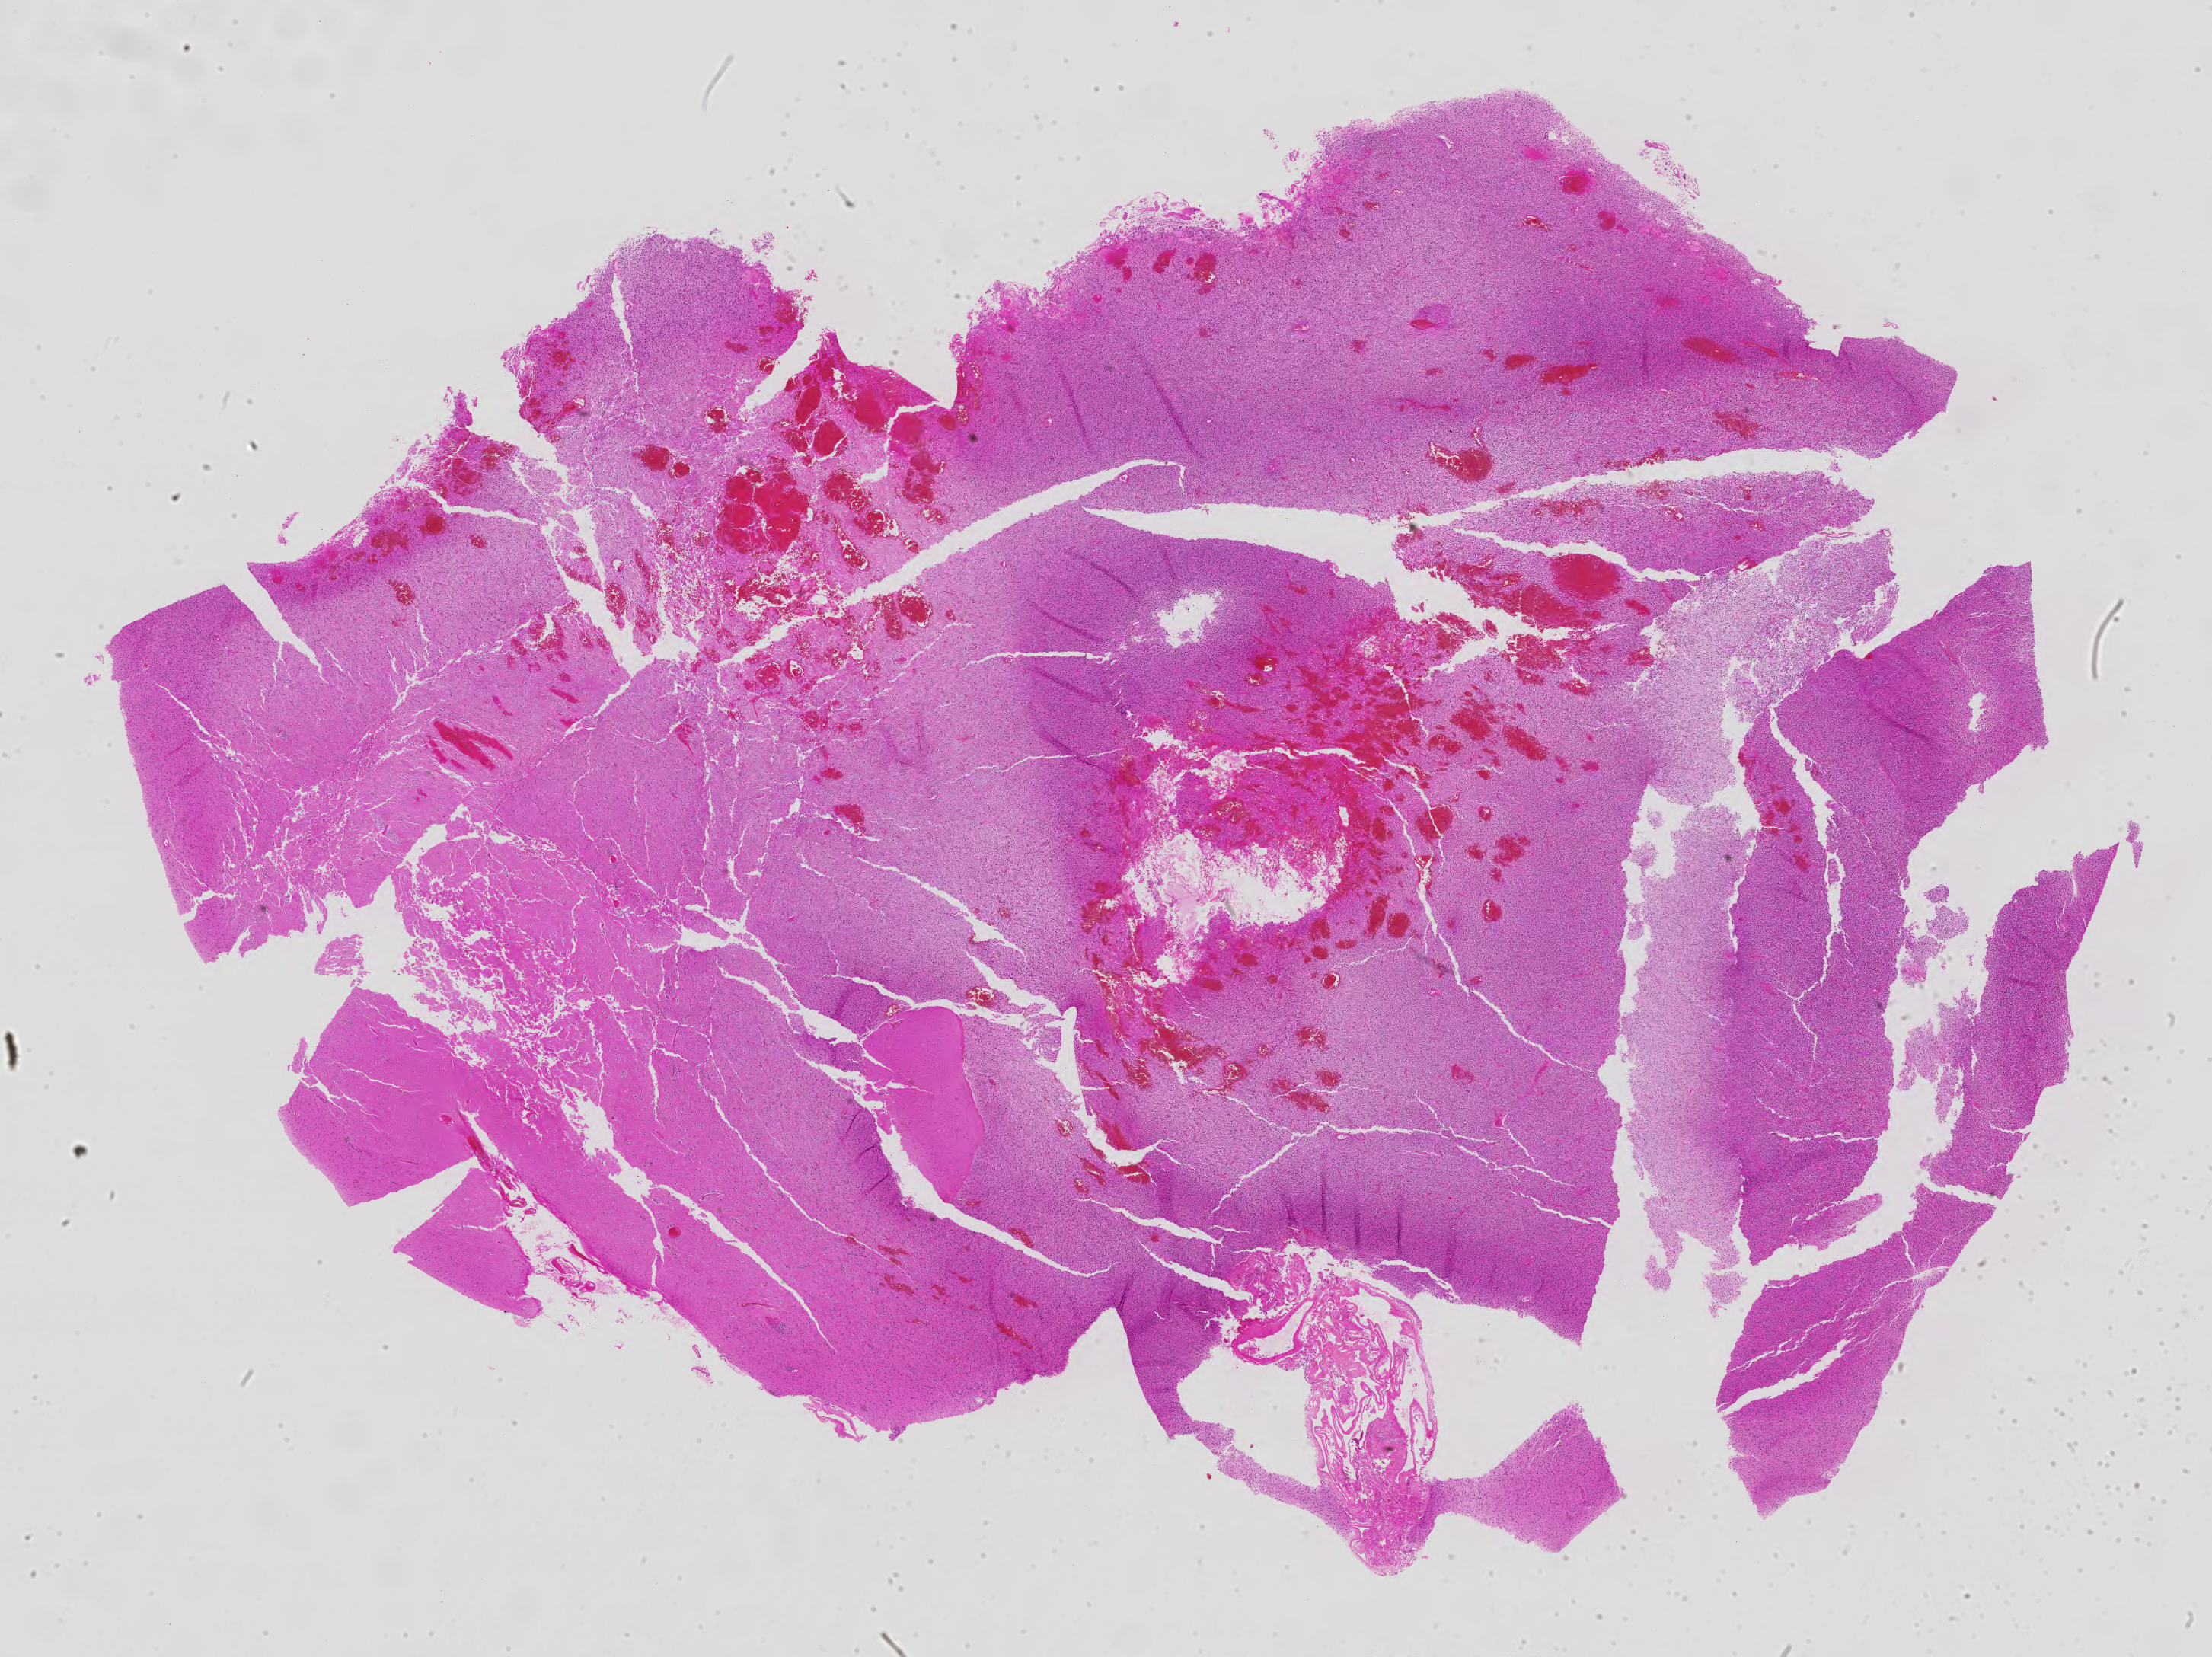
Whole-slide histology image, H&E — a low-resolution overview of the entire scanned area, about 23.2 x 17.4 mm (acquisition: 40x scan), formalin-fixed paraffin-embedded (FFPE) diagnostic section, primary tumour sample from the brain. Female patient; age at initial diagnosis 26 years. Histologic grade: G3 (poorly differentiated).
Laterality: left. Pathologic diagnosis: Mixed glioma (cerebrum).